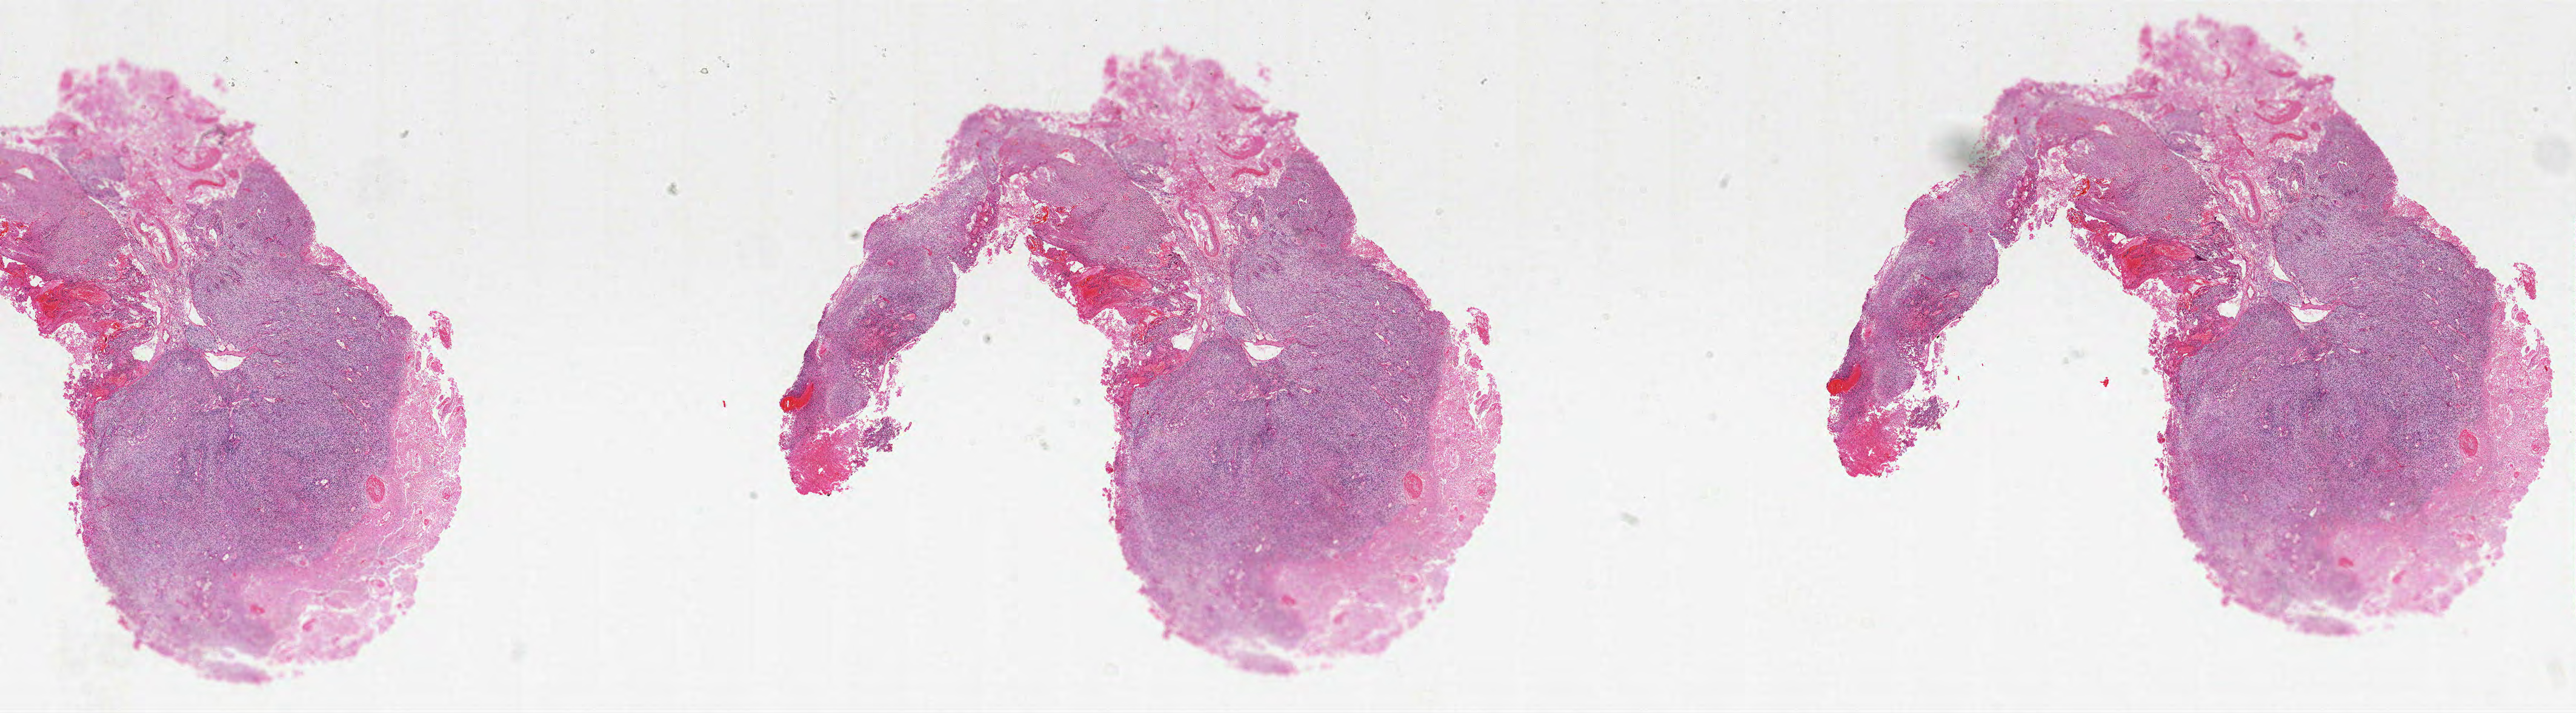
Digitized Hematoxylin and eosin (H&E) stained tissue section (whole slide) — shown as a low-resolution overview of the whole scanned area (about 34.0 x 9.4 mm, acquisition: 20x scan). Formalin-fixed paraffin-embedded (FFPE) diagnostic section. Sample: primary tumour, brain. Patient: male, age at initial diagnosis 74 years.
• histologic diagnosis: Glioblastoma